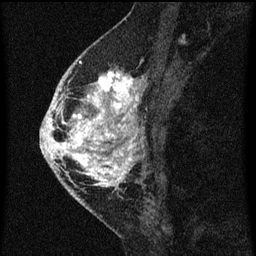
Breast MRI (dynamic contrast-enhanced), one sagittal slice; slice 27 of 60 in the series (ordered by position); dynamic contrast-enhanced series, image 2 of 3 at this slice position (ordered by acquisition); 1.5 T; TE 4.2 ms, TR 8 ms; 2 mm slice thickness; 256 × 256 image matrix, field of view 180 × 180 mm. Female patient, age 46 years.
Outlined on this slice (semi-automatically segmented with operator editing):
- analysis volume of interest (the breast-tissue region the enhancement analysis was run in; not a lesion): box from (x=48, y=68) to (x=145, y=195) px
- tumour enhancement mask (voxels above the 70 % enhancement threshold inside the analysis volume of interest): (x=48, y=72)–(x=145, y=195)